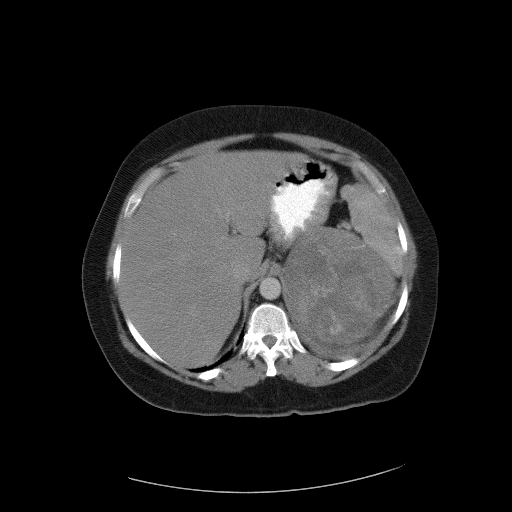
Contrast-enhanced abdominal CT, one axial slice. Slice 76 of 90 in the series (ordered by position). 120 kVp. Intravenous contrast given. Soft-tissue window (W 400 / L 40 HU). 5 mm slice thickness. 512 × 512 image matrix, field of view 480 × 480 mm. Patient: female, 55 years. Case-level facts recorded for this patient, not image findings: diagnosis: adrenocortical carcinoma; tumour side: left adrenal.
Outlined on this slice (semi-automatically segmented with operator editing):
- mass: bounding box <286,230,392,343> (left, top, right, bottom; pixels)